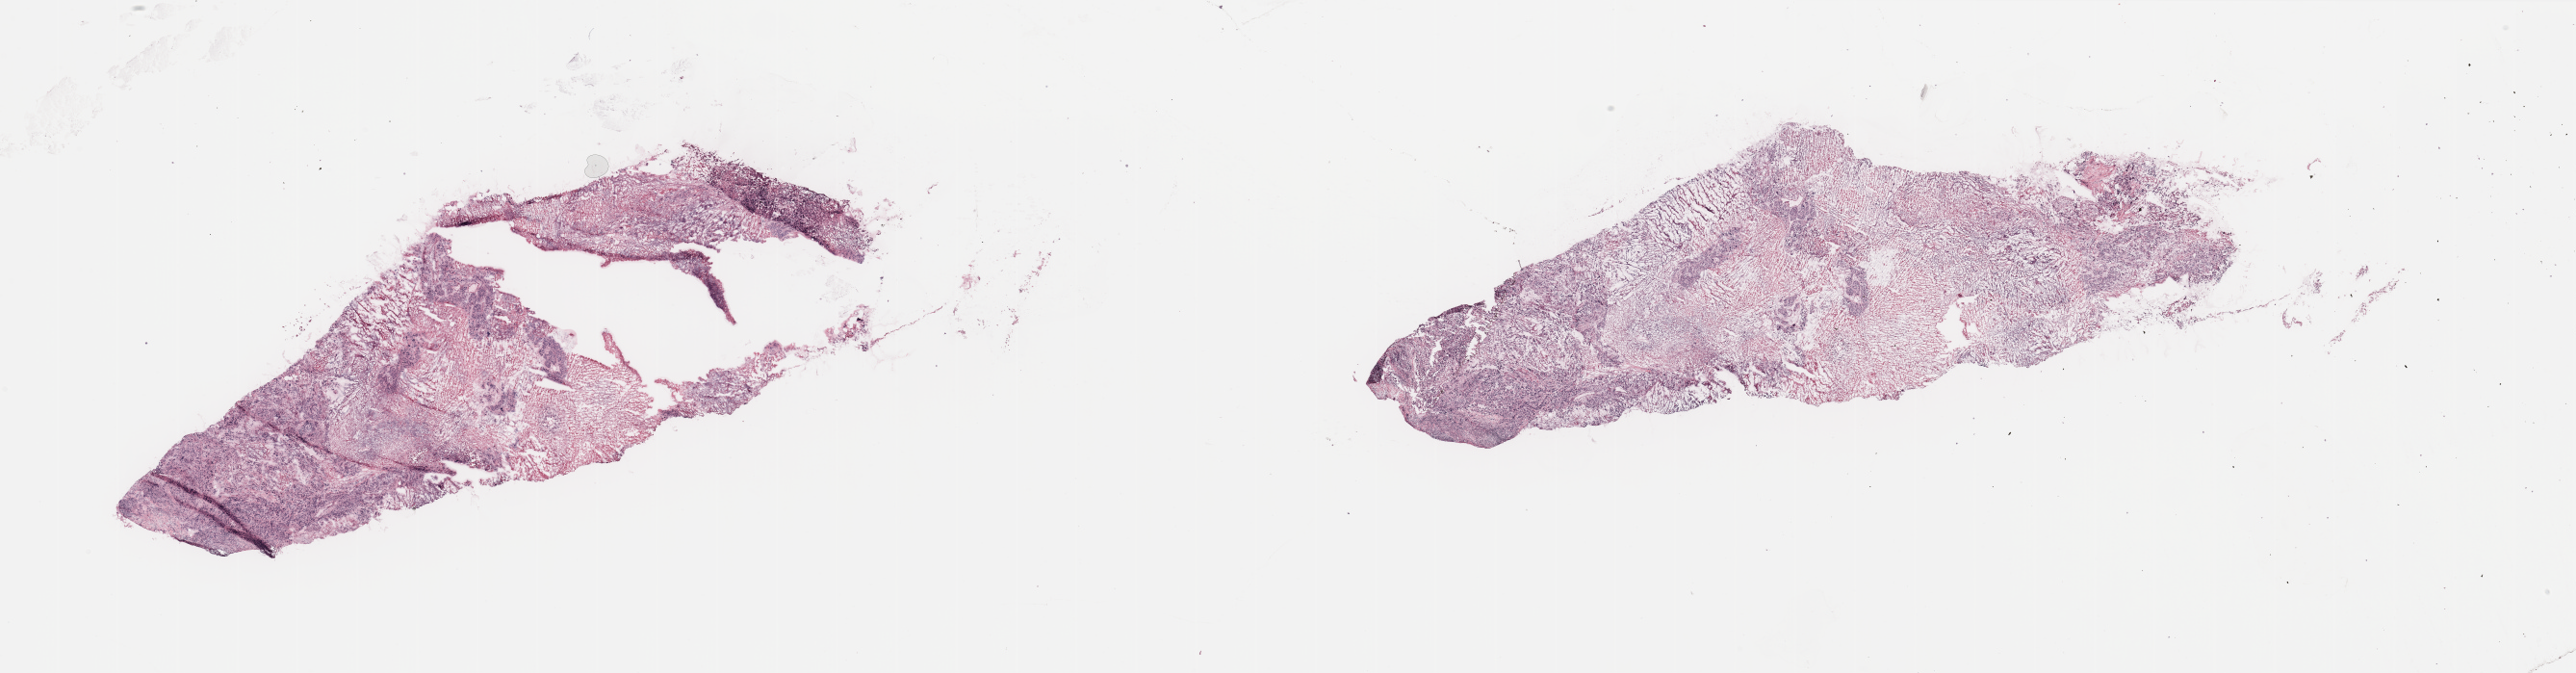
Digitized H&E-stained tissue section (whole slide), low-resolution overview of the scanned area, about 42.3 x 11.1 mm. Breast, tissue type not recorded.
Patient diagnosis (cohort enrolment): breast cancer (breast).